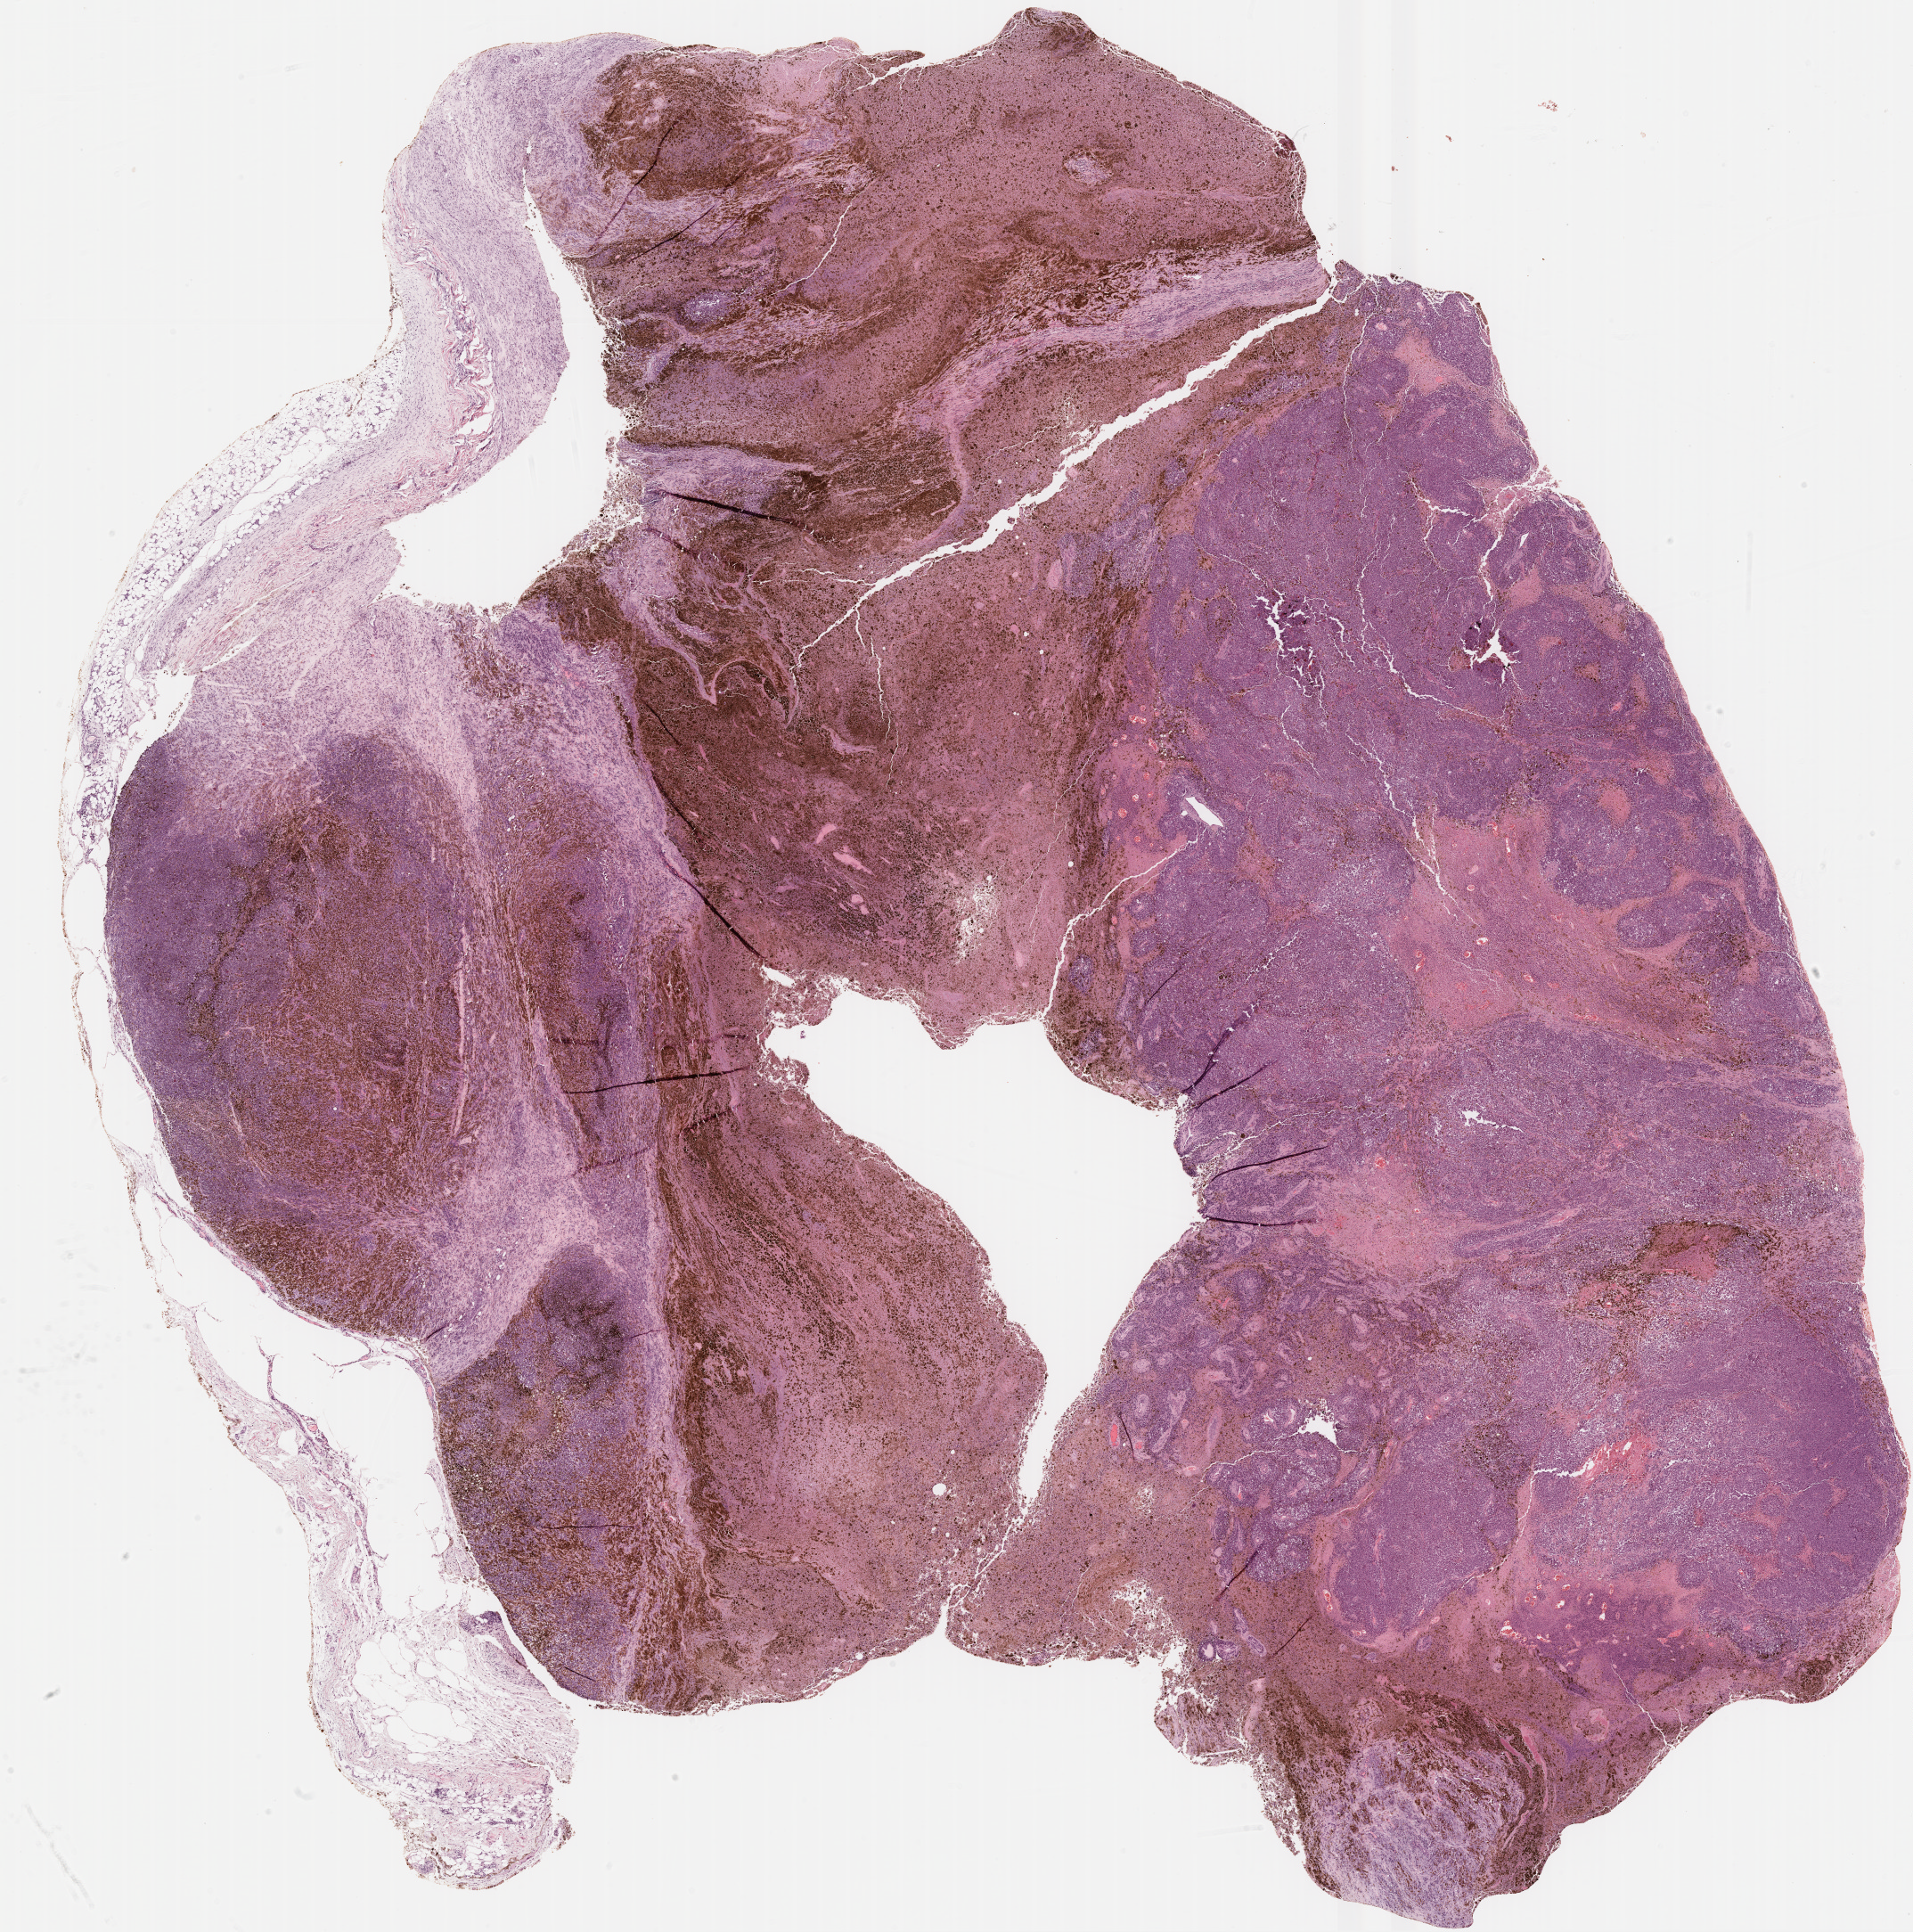
H&E whole-slide image, whole scanned area (about 17.3 x 17.5 mm) shown as a low-resolution overview; formalin-fixed paraffin-embedded (FFPE) diagnostic section; metastatic tumour sample, sampled site not recorded. Patient: female, age at initial diagnosis 70 years.
This section: metastatic tumour tissue. Patient diagnosis: Malignant melanoma, NOS.